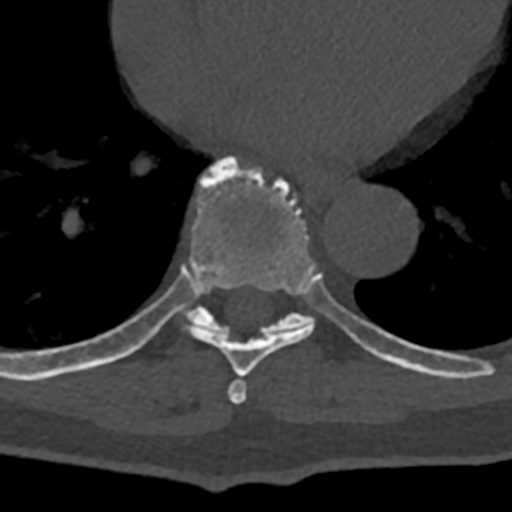
CT including the spine, one axial slice. Position 692 of 797 along the scan axis. Bone window (W 1800 / L 400 HU). 0.5 mm slice thickness. 512 × 512 image matrix, field of view 160 × 160 mm. Male patient, age 74 years. Case-level facts recorded for this patient, not image findings: primary cancer: renal; vertebrae with lytic lesions (as recorded): T10, L1, L2, L3, L4, L5.
Structures marked on this image (semi-automatic segmentation, software-assisted and operator-edited):
- T7 vertebra: box from (x=228, y=378) to (x=247, y=404) px
- T8 vertebra: (x=70, y=157)–(x=389, y=376)
- T9 vertebra: (x=106, y=267)–(x=432, y=375)